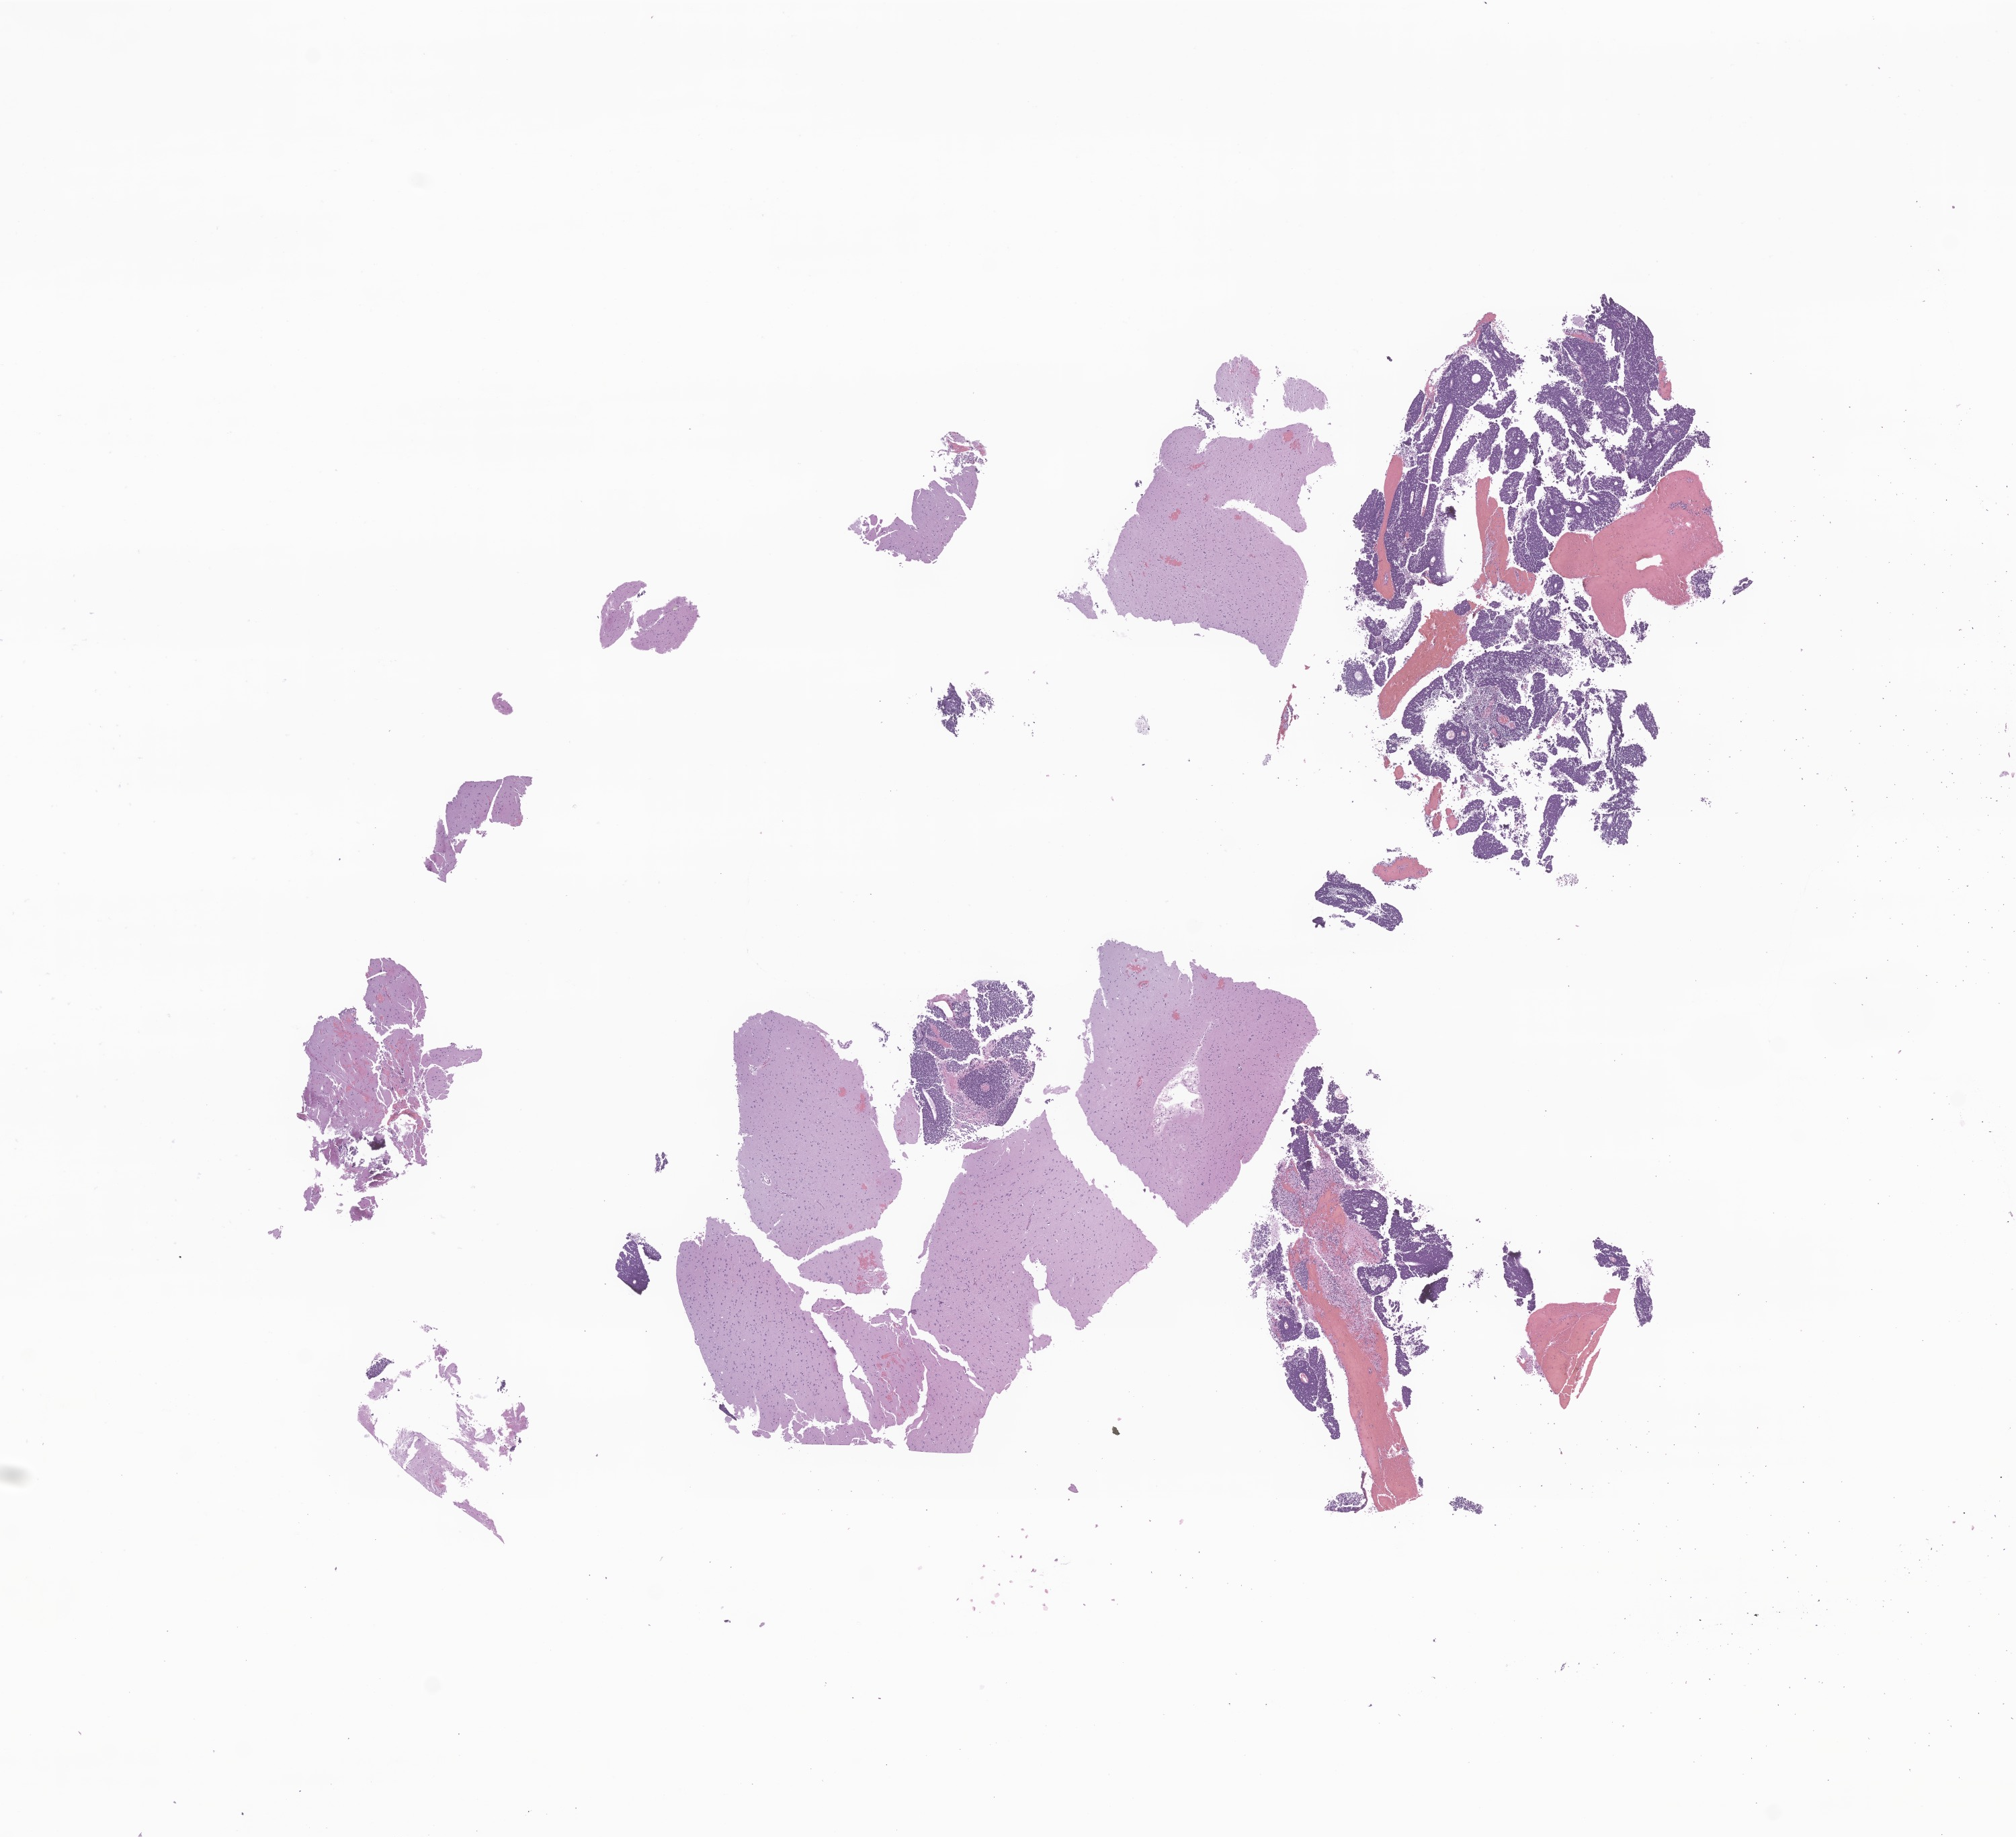
Whole-slide image, hematoxylin and eosin (H&E) stain of tumor tissue from the brain — shown as a low-resolution overview of the whole scanned area (about 12.6 x 11.5 mm); FFPE section. Patient: female, age 57 months (4 years 9 months).
Diagnosis (ICD-O-3 morphology term): Pineoblastoma.